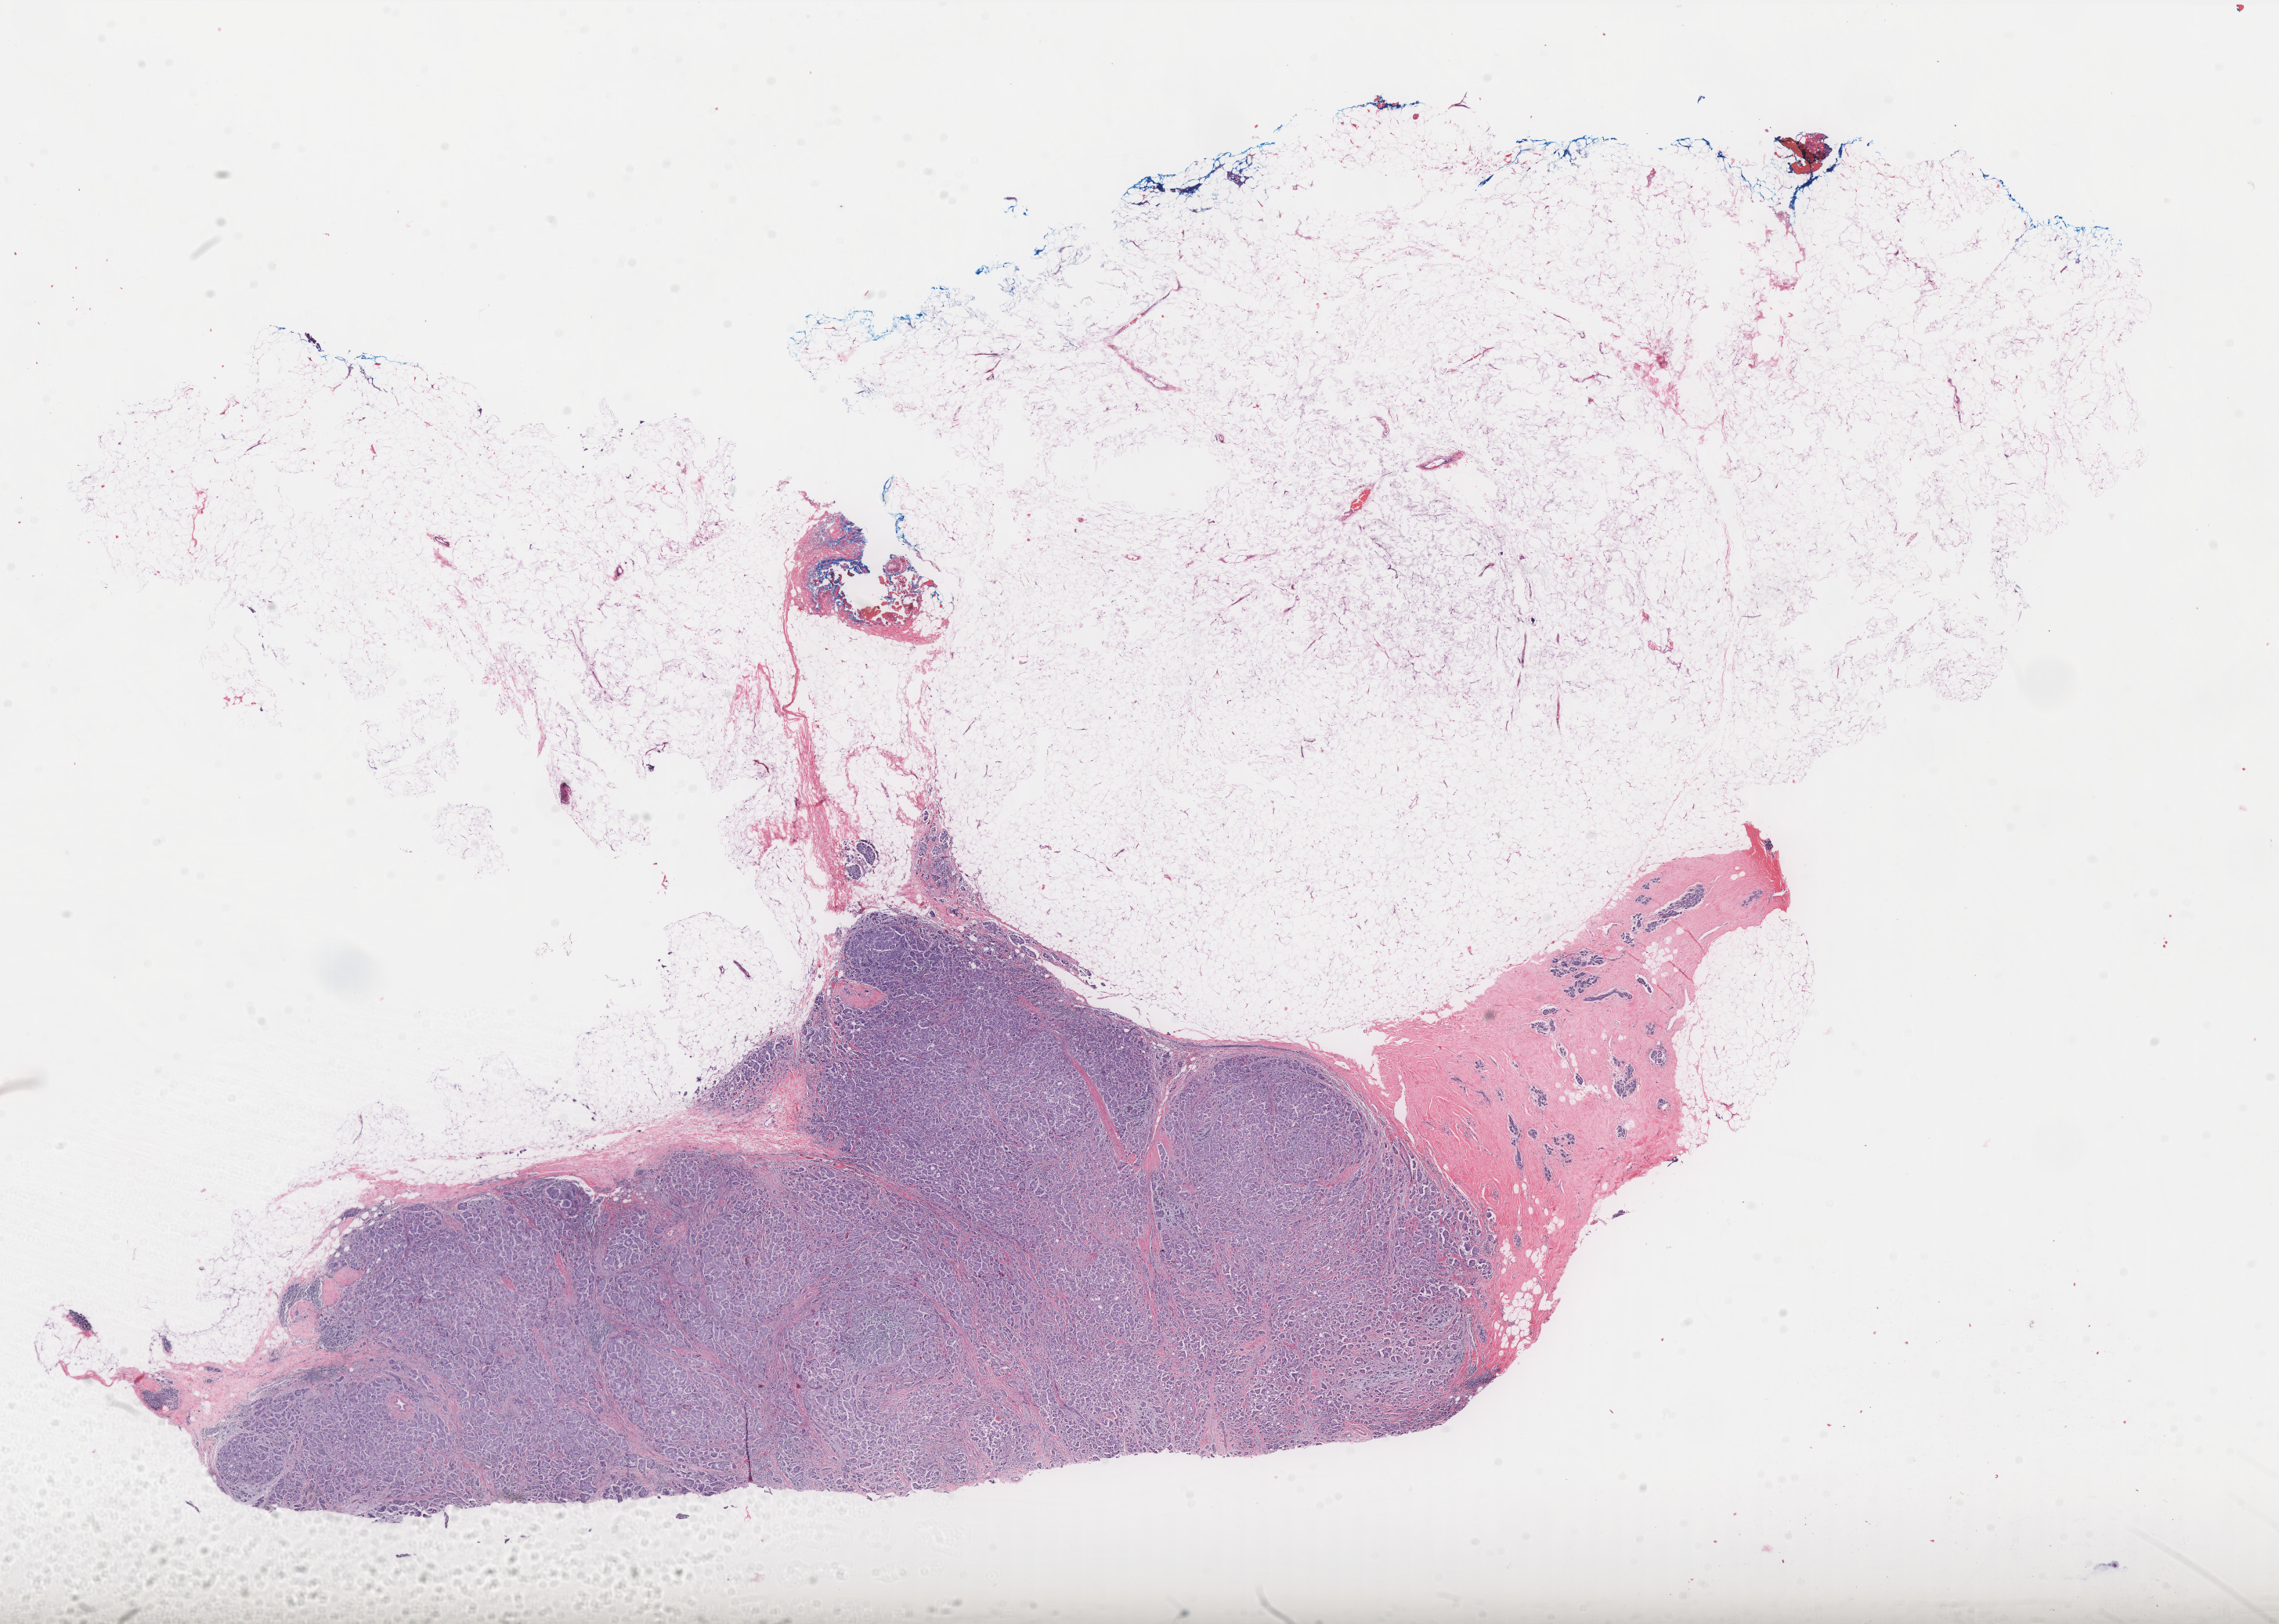
H&E-stained whole-slide image, whole scanned area (about 23.3 x 16.6 mm) shown as a low-resolution overview; FFPE section; breast, primary tumour sample. Patient: female, age at initial diagnosis 53 years.
Lymph nodes positive (case pathology): 1 of 13 examined. Pathologic diagnosis: Infiltrating duct carcinoma, NOS. Laterality: right. AJCC pathologic stage: IIB (6th edition).